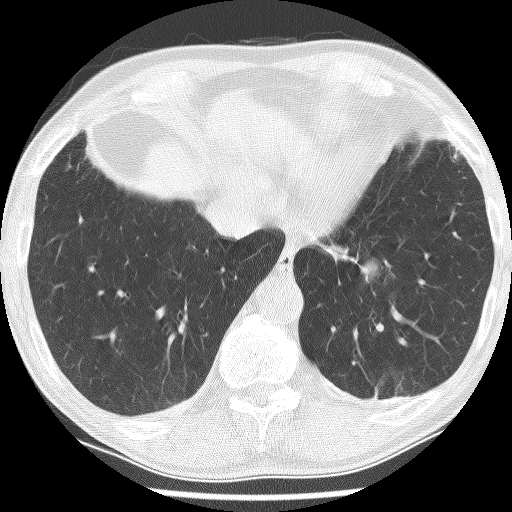
Low-dose screening chest CT, one axial slice; position 38 of 226 along the scan axis; reconstruction kernel BONE; 120 kVp; lung window (W 1500 / L -600 HU); 2.5 mm slice thickness; 512 × 512 image matrix, field of view 320 × 320 mm.
Structures marked on this image (expert manual segmentation):
- lesion 1 (tumor, lower lobe of left lung): box from (x=359, y=261) to (x=380, y=282) px